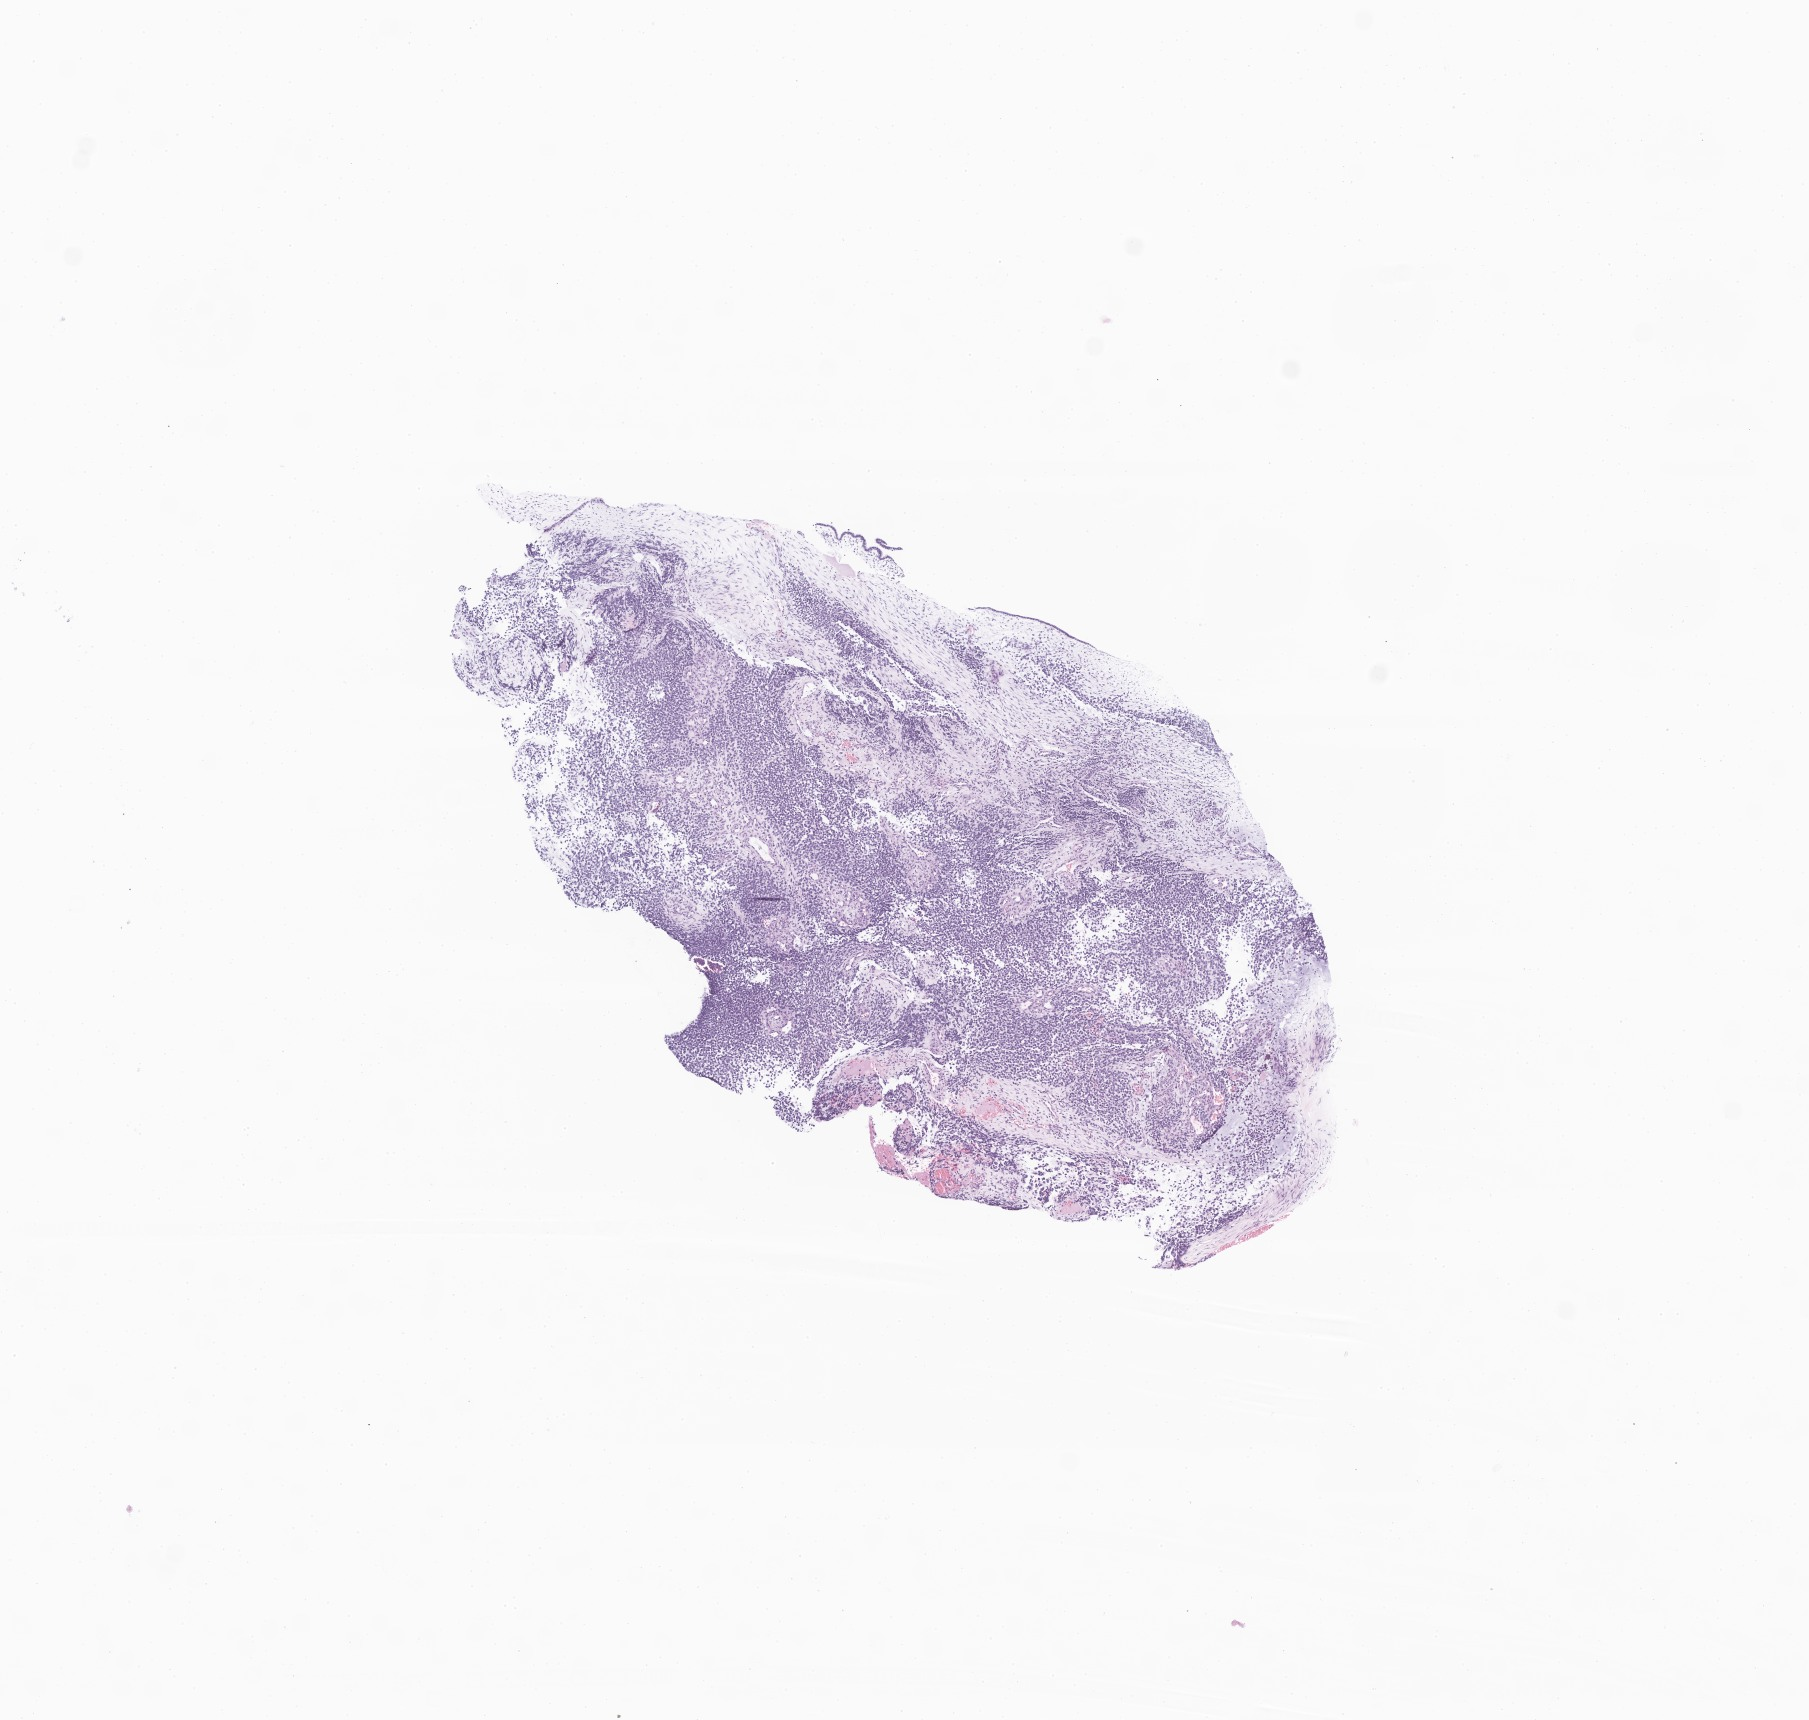
Digitized haematoxylin and eosin-stained section of tumor tissue from the nasopharynx — shown as a low-resolution overview of the whole scanned area (about 7.6 x 7.3 mm); formalin-fixed paraffin-embedded section. Female patient, age 114 months (9 years 6 months).
Diagnosis: Embryonal rhabdomyosarcoma, NOS.